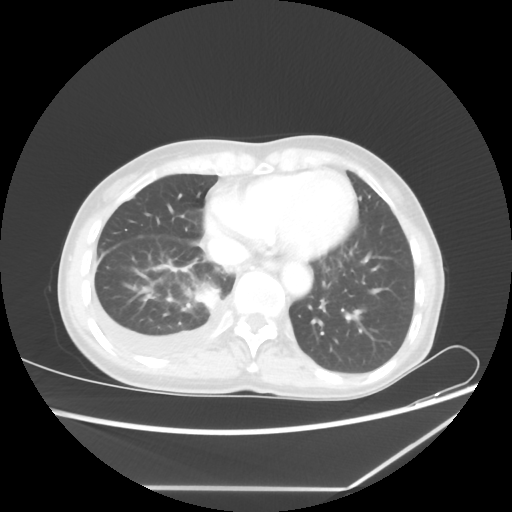
Chest CT, one axial slice. Slice 19 of 60 in the series (ordered by position). Lung window (W 1500 / L -600 HU). 5 mm slice thickness. 512 × 512 image matrix, field of view 364 × 364 mm. Female patient, age 59 years. Case-level facts recorded for this patient, not image findings: clinical TNM (as recorded): T1c N1 M1.
Annotated regions visible in this slice (bounding box drawn by a radiologist):
- lung tumour (recorded histology: adenocarcinoma): bounding box <192,283,220,312> (left, top, right, bottom; pixels)